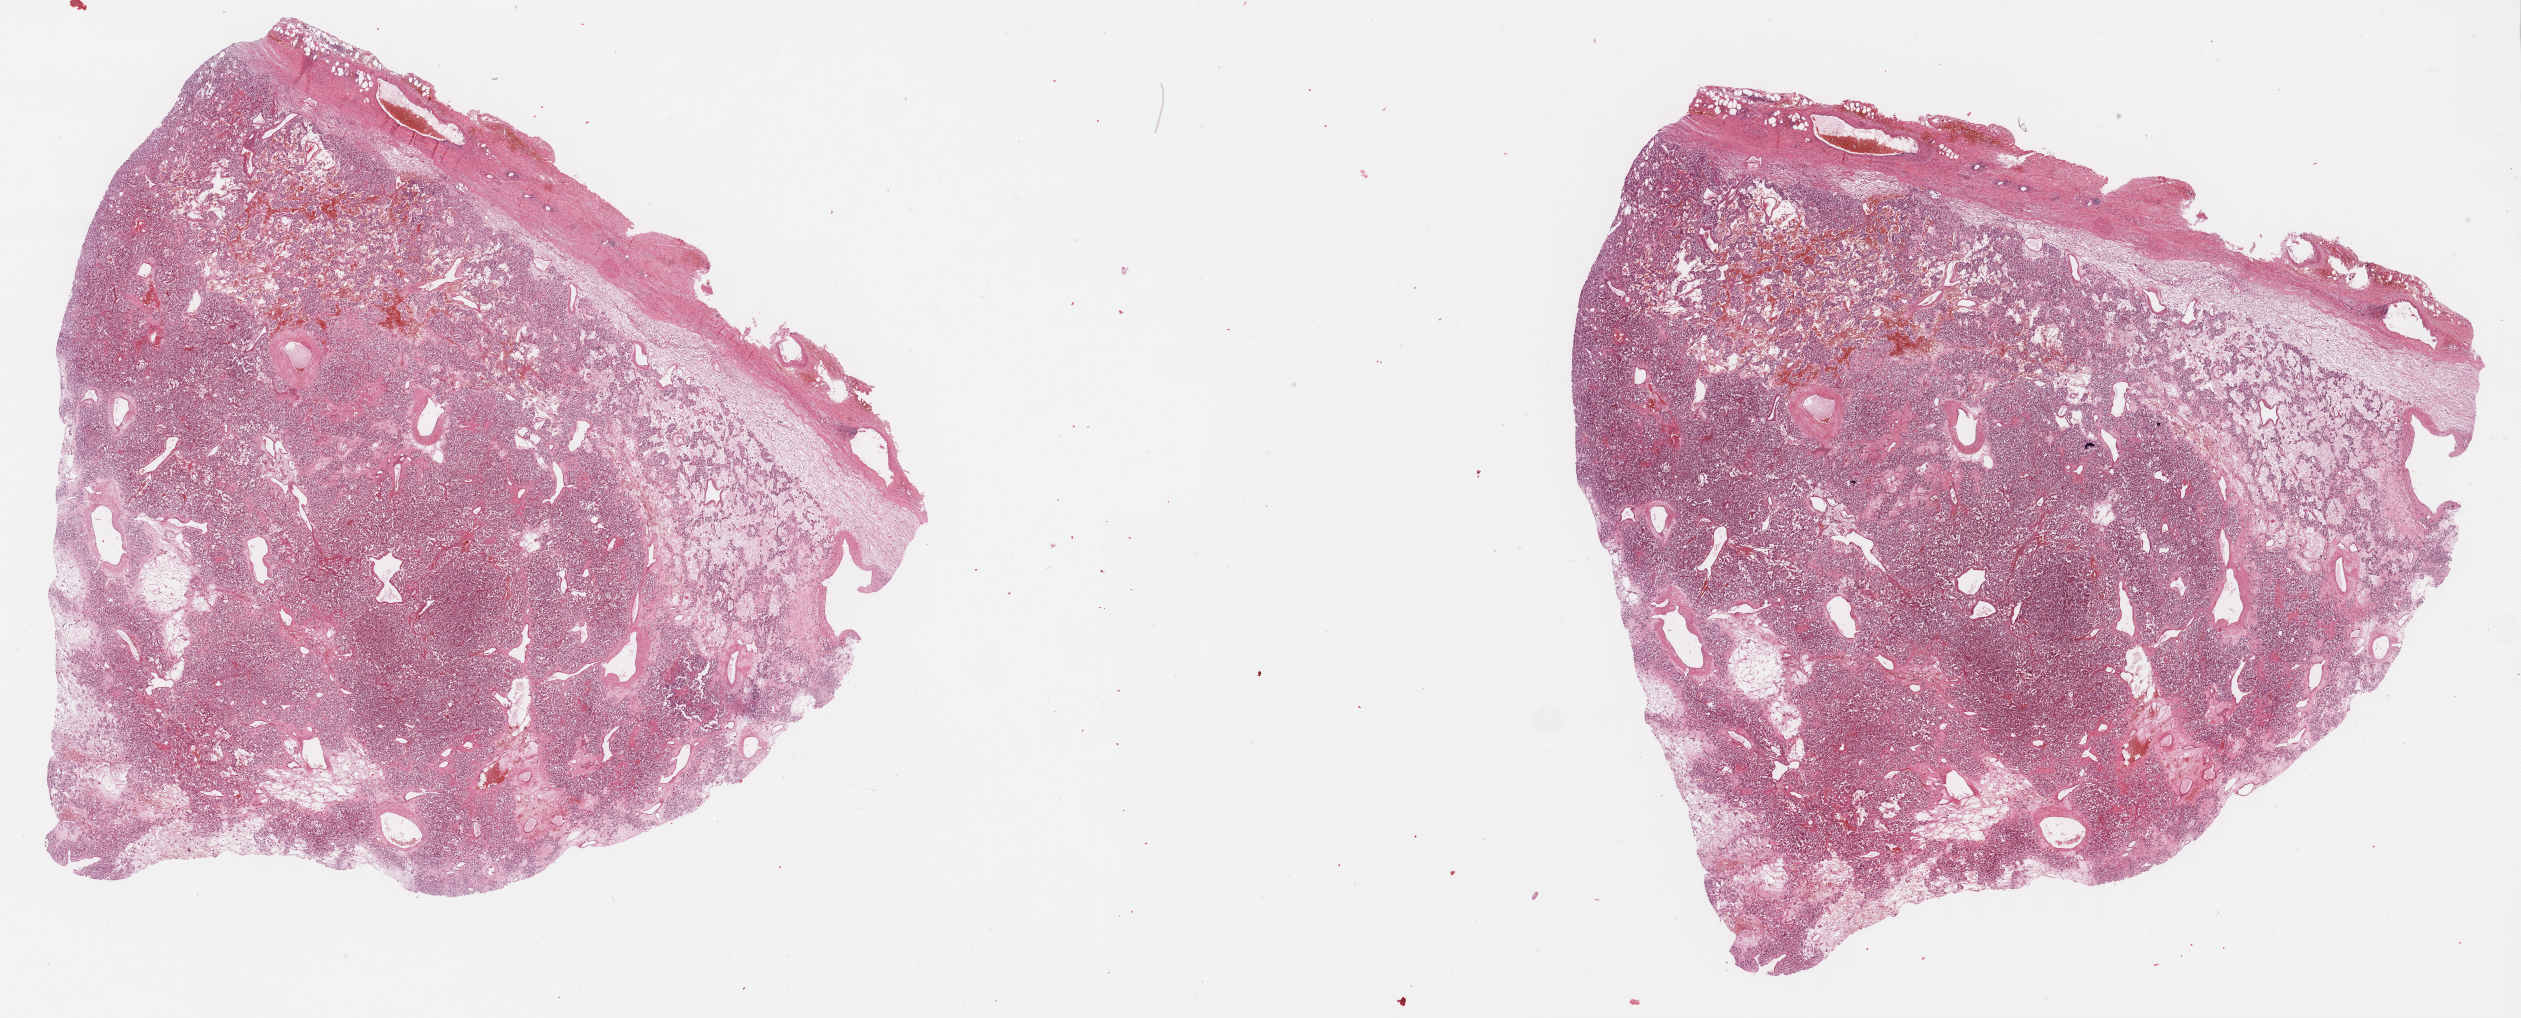
H&E whole-slide image, whole scanned area (about 40.8 x 16.5 mm, slide scanned at 40x) shown as a low-resolution overview, FFPE section, primary tumour sample from the connective, subcutaneous and other soft tissues. Patient: female, age at initial diagnosis 75 years.
Pathologic diagnosis: Extra-adrenal paraganglioma, NOS (connective, subcutaneous and other soft tissues of pelvis).